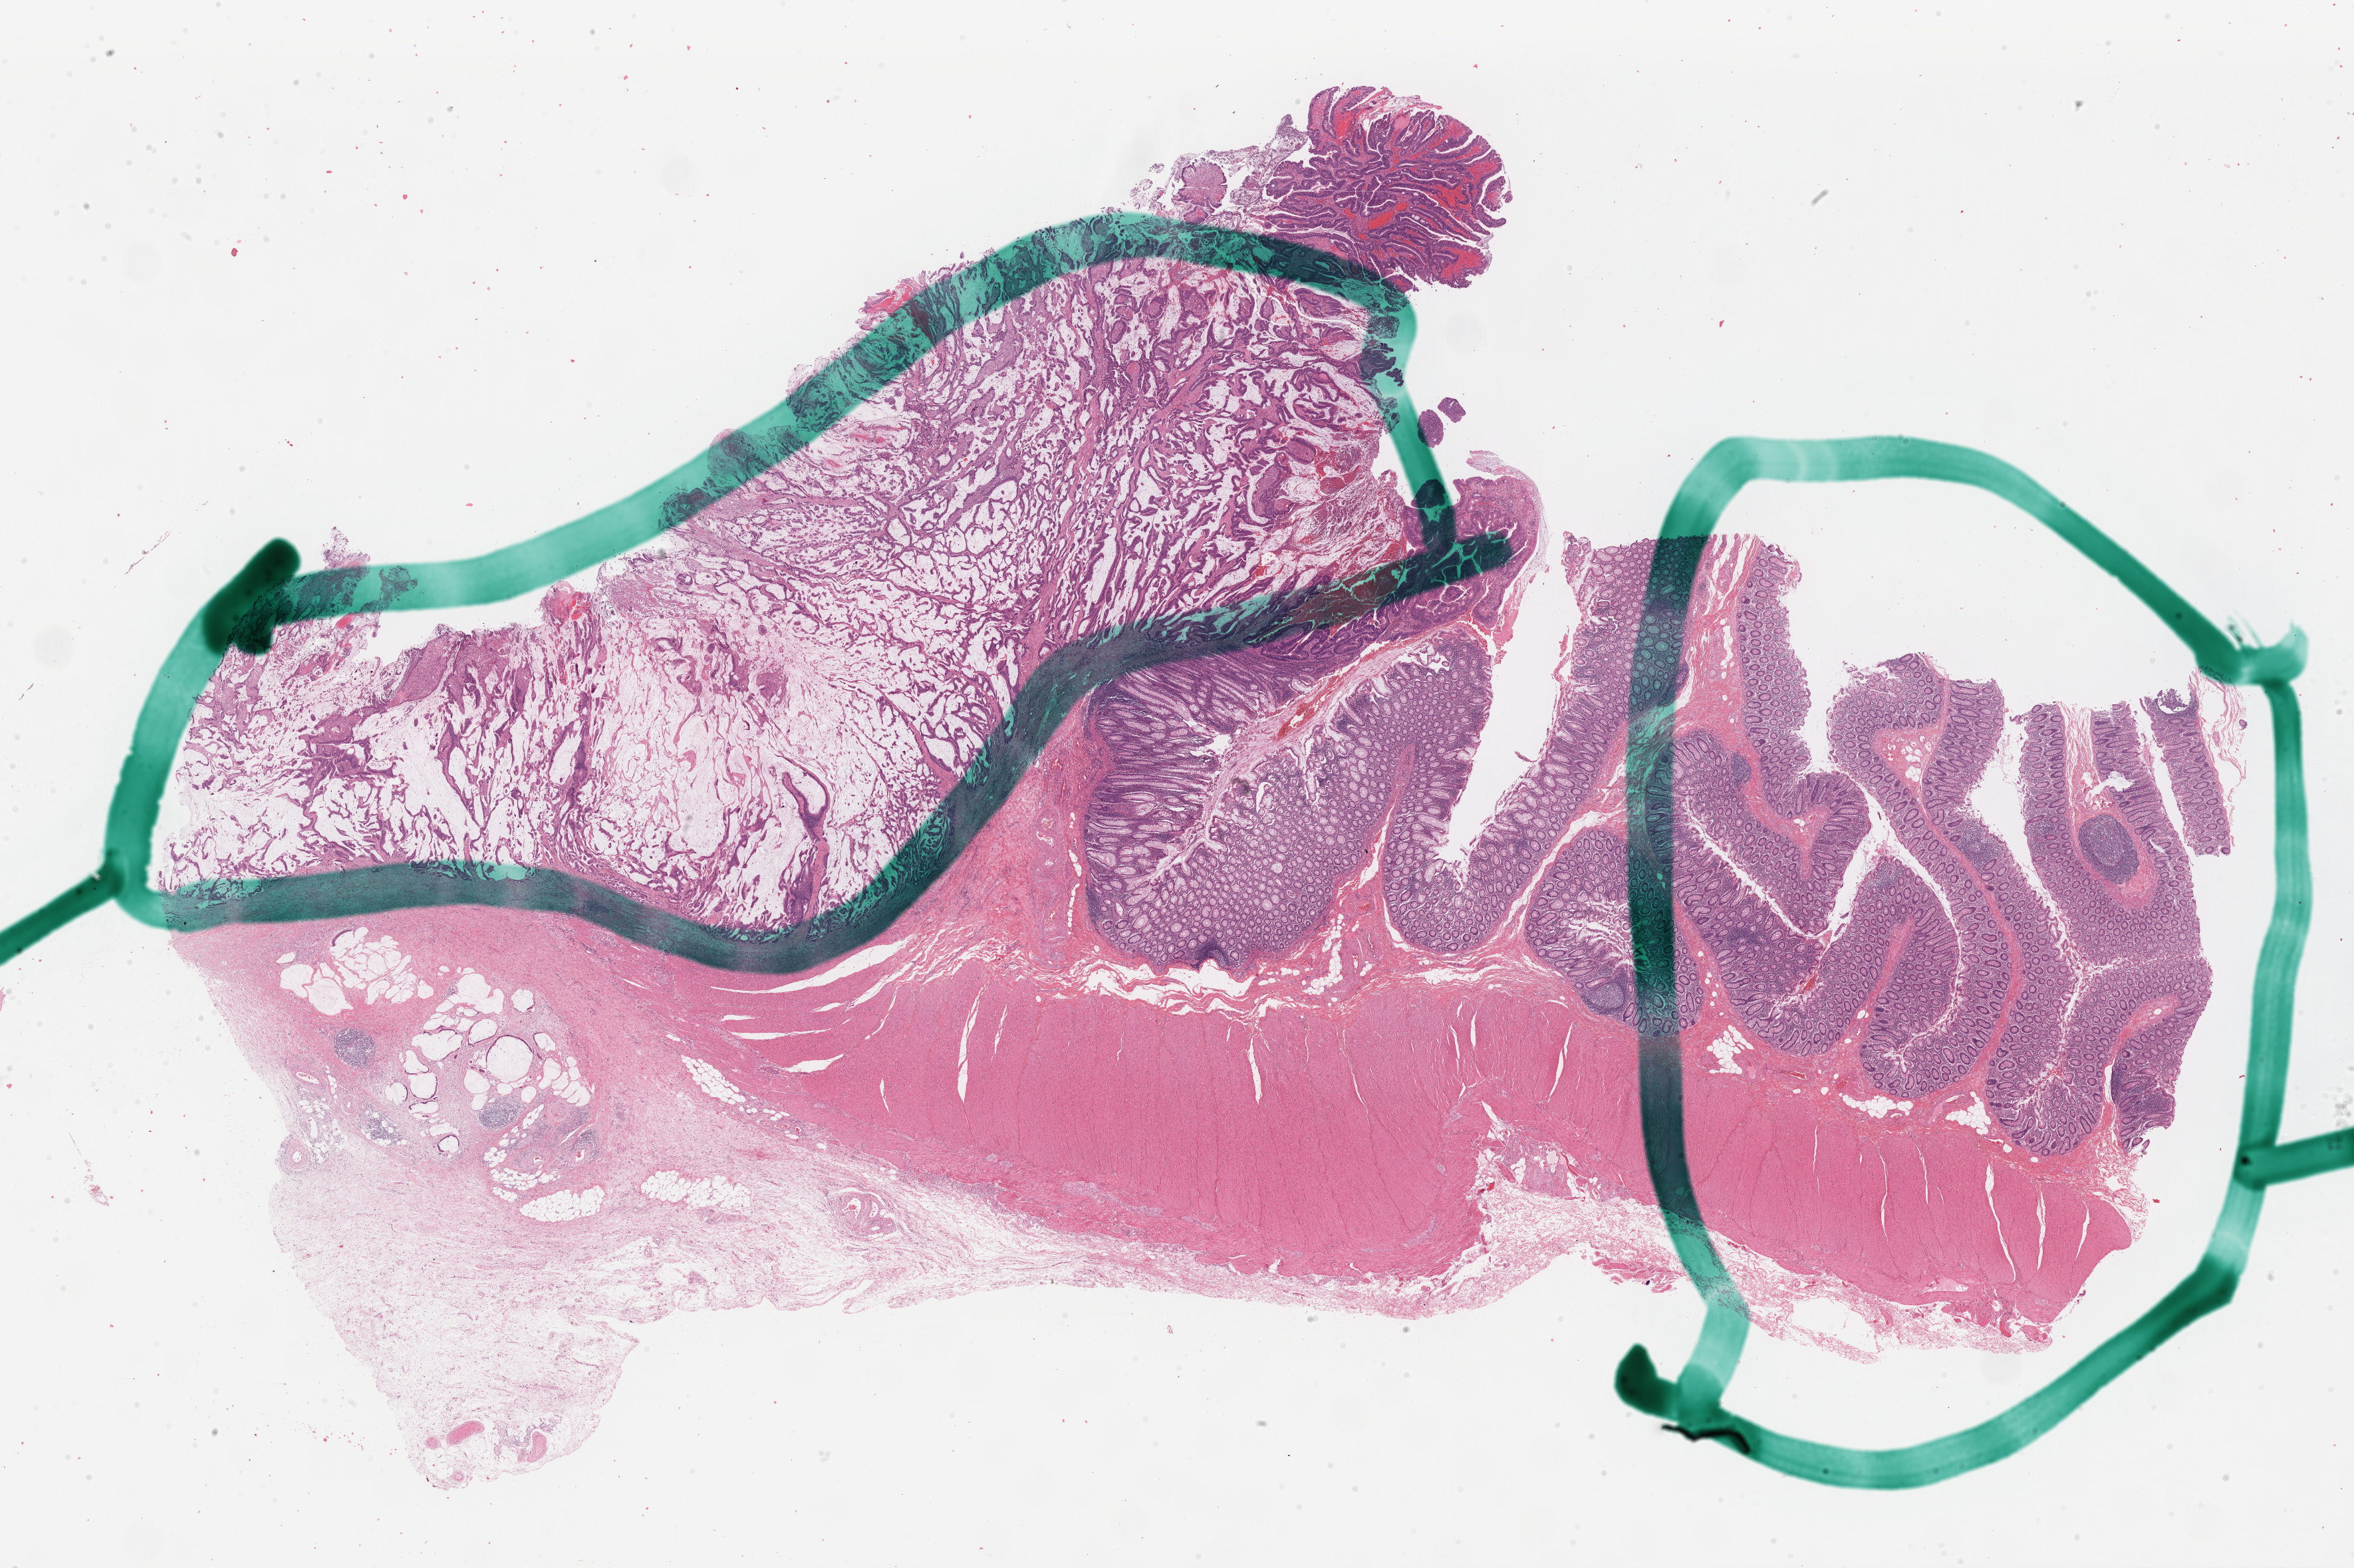
Whole-slide histology image, Hematoxylin and eosin (H&E) stained — whole scanned area (about 28.0 x 18.6 mm, slide scanned at 40x) shown as a low-resolution overview, FFPE section, sample: primary tumour, colon. Patient sex: male.
AJCC pathologic stage: IIA. Histologic diagnosis: Mucinous adenocarcinoma (splenic flexure of colon). Lymph nodes positive (case pathology): 0 of 6 examined.